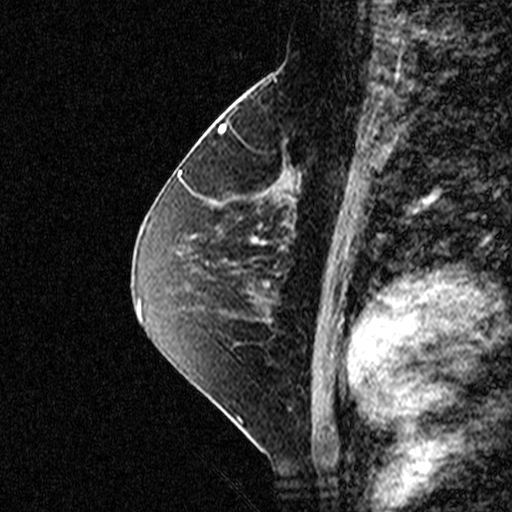
Breast MRI (dynamic contrast-enhanced), one sagittal slice; slice 21 of 44 in the series (ordered by position); dynamic contrast-enhanced study with each time point stored as its own series, time point 2 of 3 at this slice position (early post-contrast, ordered by acquisition time); 1.5 T; TE 4.5 ms, TR 11 ms; 512 × 512 image matrix, field of view 200 × 200 mm. Female patient, age 49 years. From the clinical record (not read from this slice): setting: breast cancer imaged before/during neoadjuvant chemotherapy; receptor status: triple-negative.
Outlined on this slice (semi-automatic segmentation, software-assisted and operator-edited):
- analysis volume of interest (the breast-tissue region the enhancement analysis was run in; not a lesion): bounding box (x1, y1, x2, y2) in pixels: (254, 112, 347, 207)
- tumour enhancement mask (voxels above the 90 % enhancement threshold inside the analysis volume of interest): (282, 158, 347, 202)